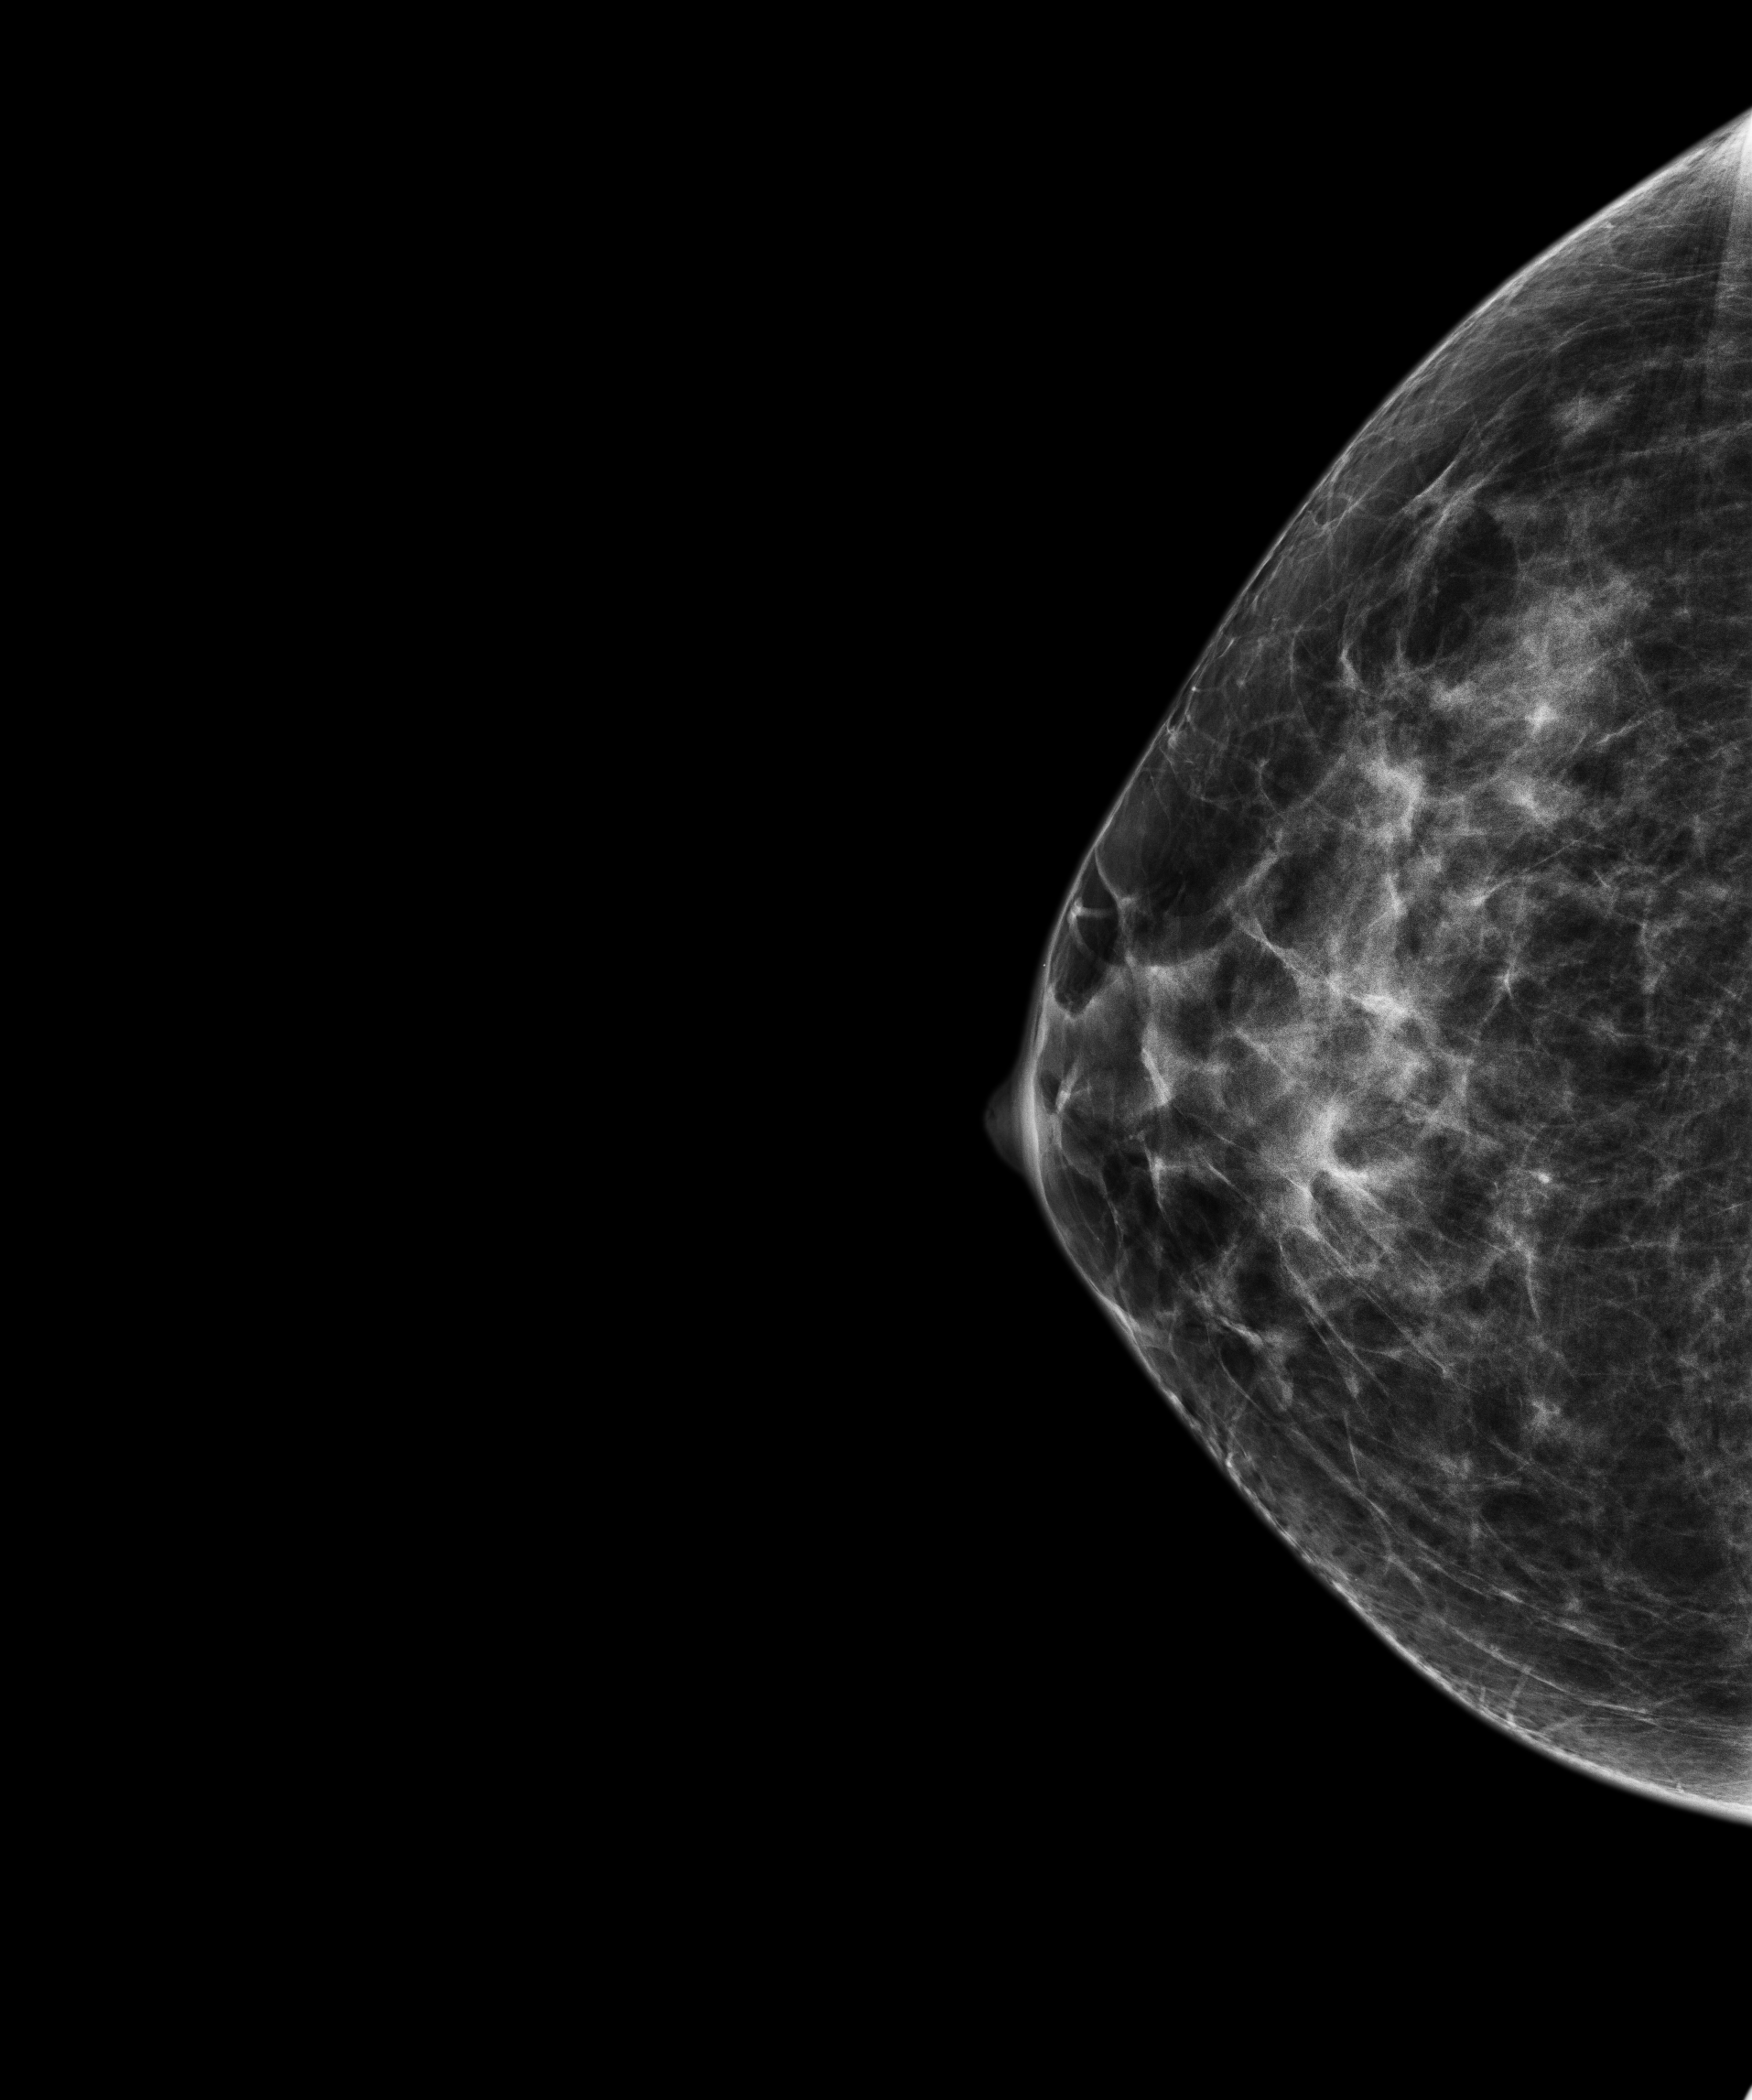
Screening examination, system: Senographe Pristina. Patient: female, 44 years.
Image type: full-field digital mammogram. Breast: right. Projection: craniocaudal (CC) view.